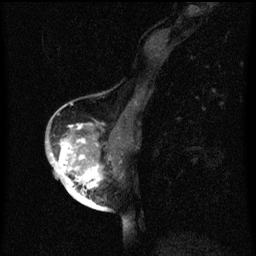
Breast MRI (dynamic contrast-enhanced), one sagittal slice. Slice 29 of 60 in the series (ordered by position). Dynamic contrast-enhanced series, image 2 of 3 at this slice position (ordered by acquisition). 1.5 T. TE 4.2 ms, TR 8 ms. 2 mm slice thickness. 256 × 256 image matrix, field of view 180 × 180 mm. Female patient, age 56 years.
Annotated regions visible in this slice (semi-automatically segmented with operator editing):
- analysis volume of interest (the breast-tissue region the enhancement analysis was run in; not a lesion): bounding box (x1, y1, x2, y2) in pixels: (54, 122, 120, 199)
- tumour enhancement mask (voxels above the 70 % enhancement threshold inside the analysis volume of interest): (54, 124, 104, 199)